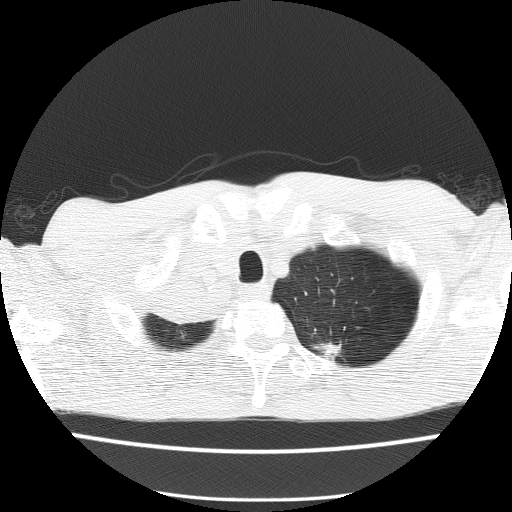
Low-dose screening chest CT, one axial slice. Slice 131 of 150 in the series (ordered by position). 120 kVp. Lung window (W 1500 / L -600 HU). 2 mm slice thickness. 512 × 512 image matrix, field of view 336 × 336 mm.
Annotated regions visible in this slice (expert manual segmentation):
- lesion 1 (tumor, hilum of right lung): bounding box (x1, y1, x2, y2) in pixels: (152, 280, 216, 323)